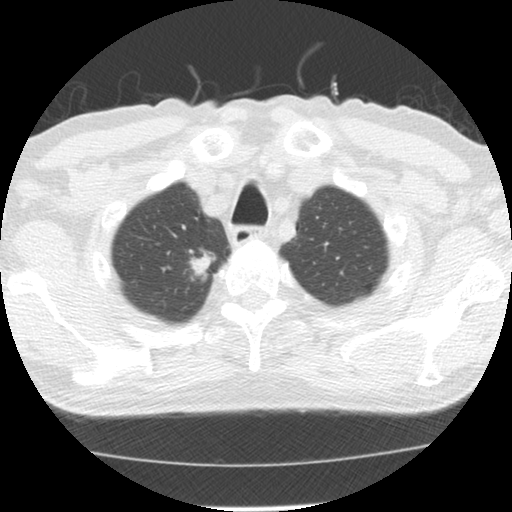
Low-dose screening chest CT, one axial slice. Position 117 of 139 along the scan axis. Reconstruction kernel STANDARD. Lung window (W 1500 / L -600 HU). 2.5 mm slice thickness. 512 × 512 image matrix.
Outlined on this slice (manually delineated by an expert):
- lesion 1 (tumor, upper lobe of right lung): bounding box <189,249,215,281> (left, top, right, bottom; pixels)